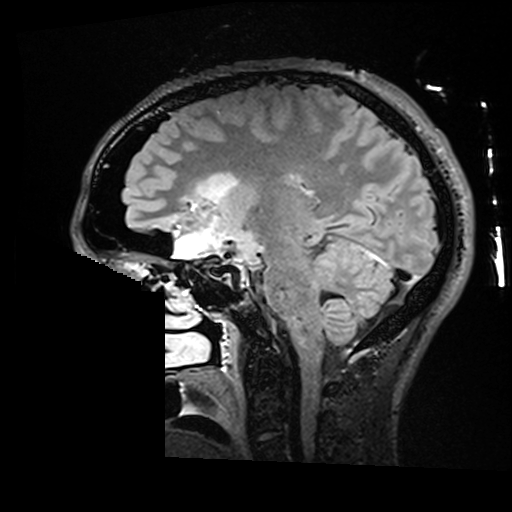
Brain MRI from a brain-tumour surgery series, one sagittal slice. Position 97 of 176 along the scan axis. T2 FLAIR. 512 × 512 image matrix, field of view 250 × 250 mm. From the clinical record (not read from this slice): histopathology: Astrocytoma; WHO grade: 2; IDH mutation: yes; tumour location: Right Insular.
Annotated regions visible in this slice (expert manual segmentation):
- residual tumour: bounding box <198,172,238,203> (left, top, right, bottom; pixels)